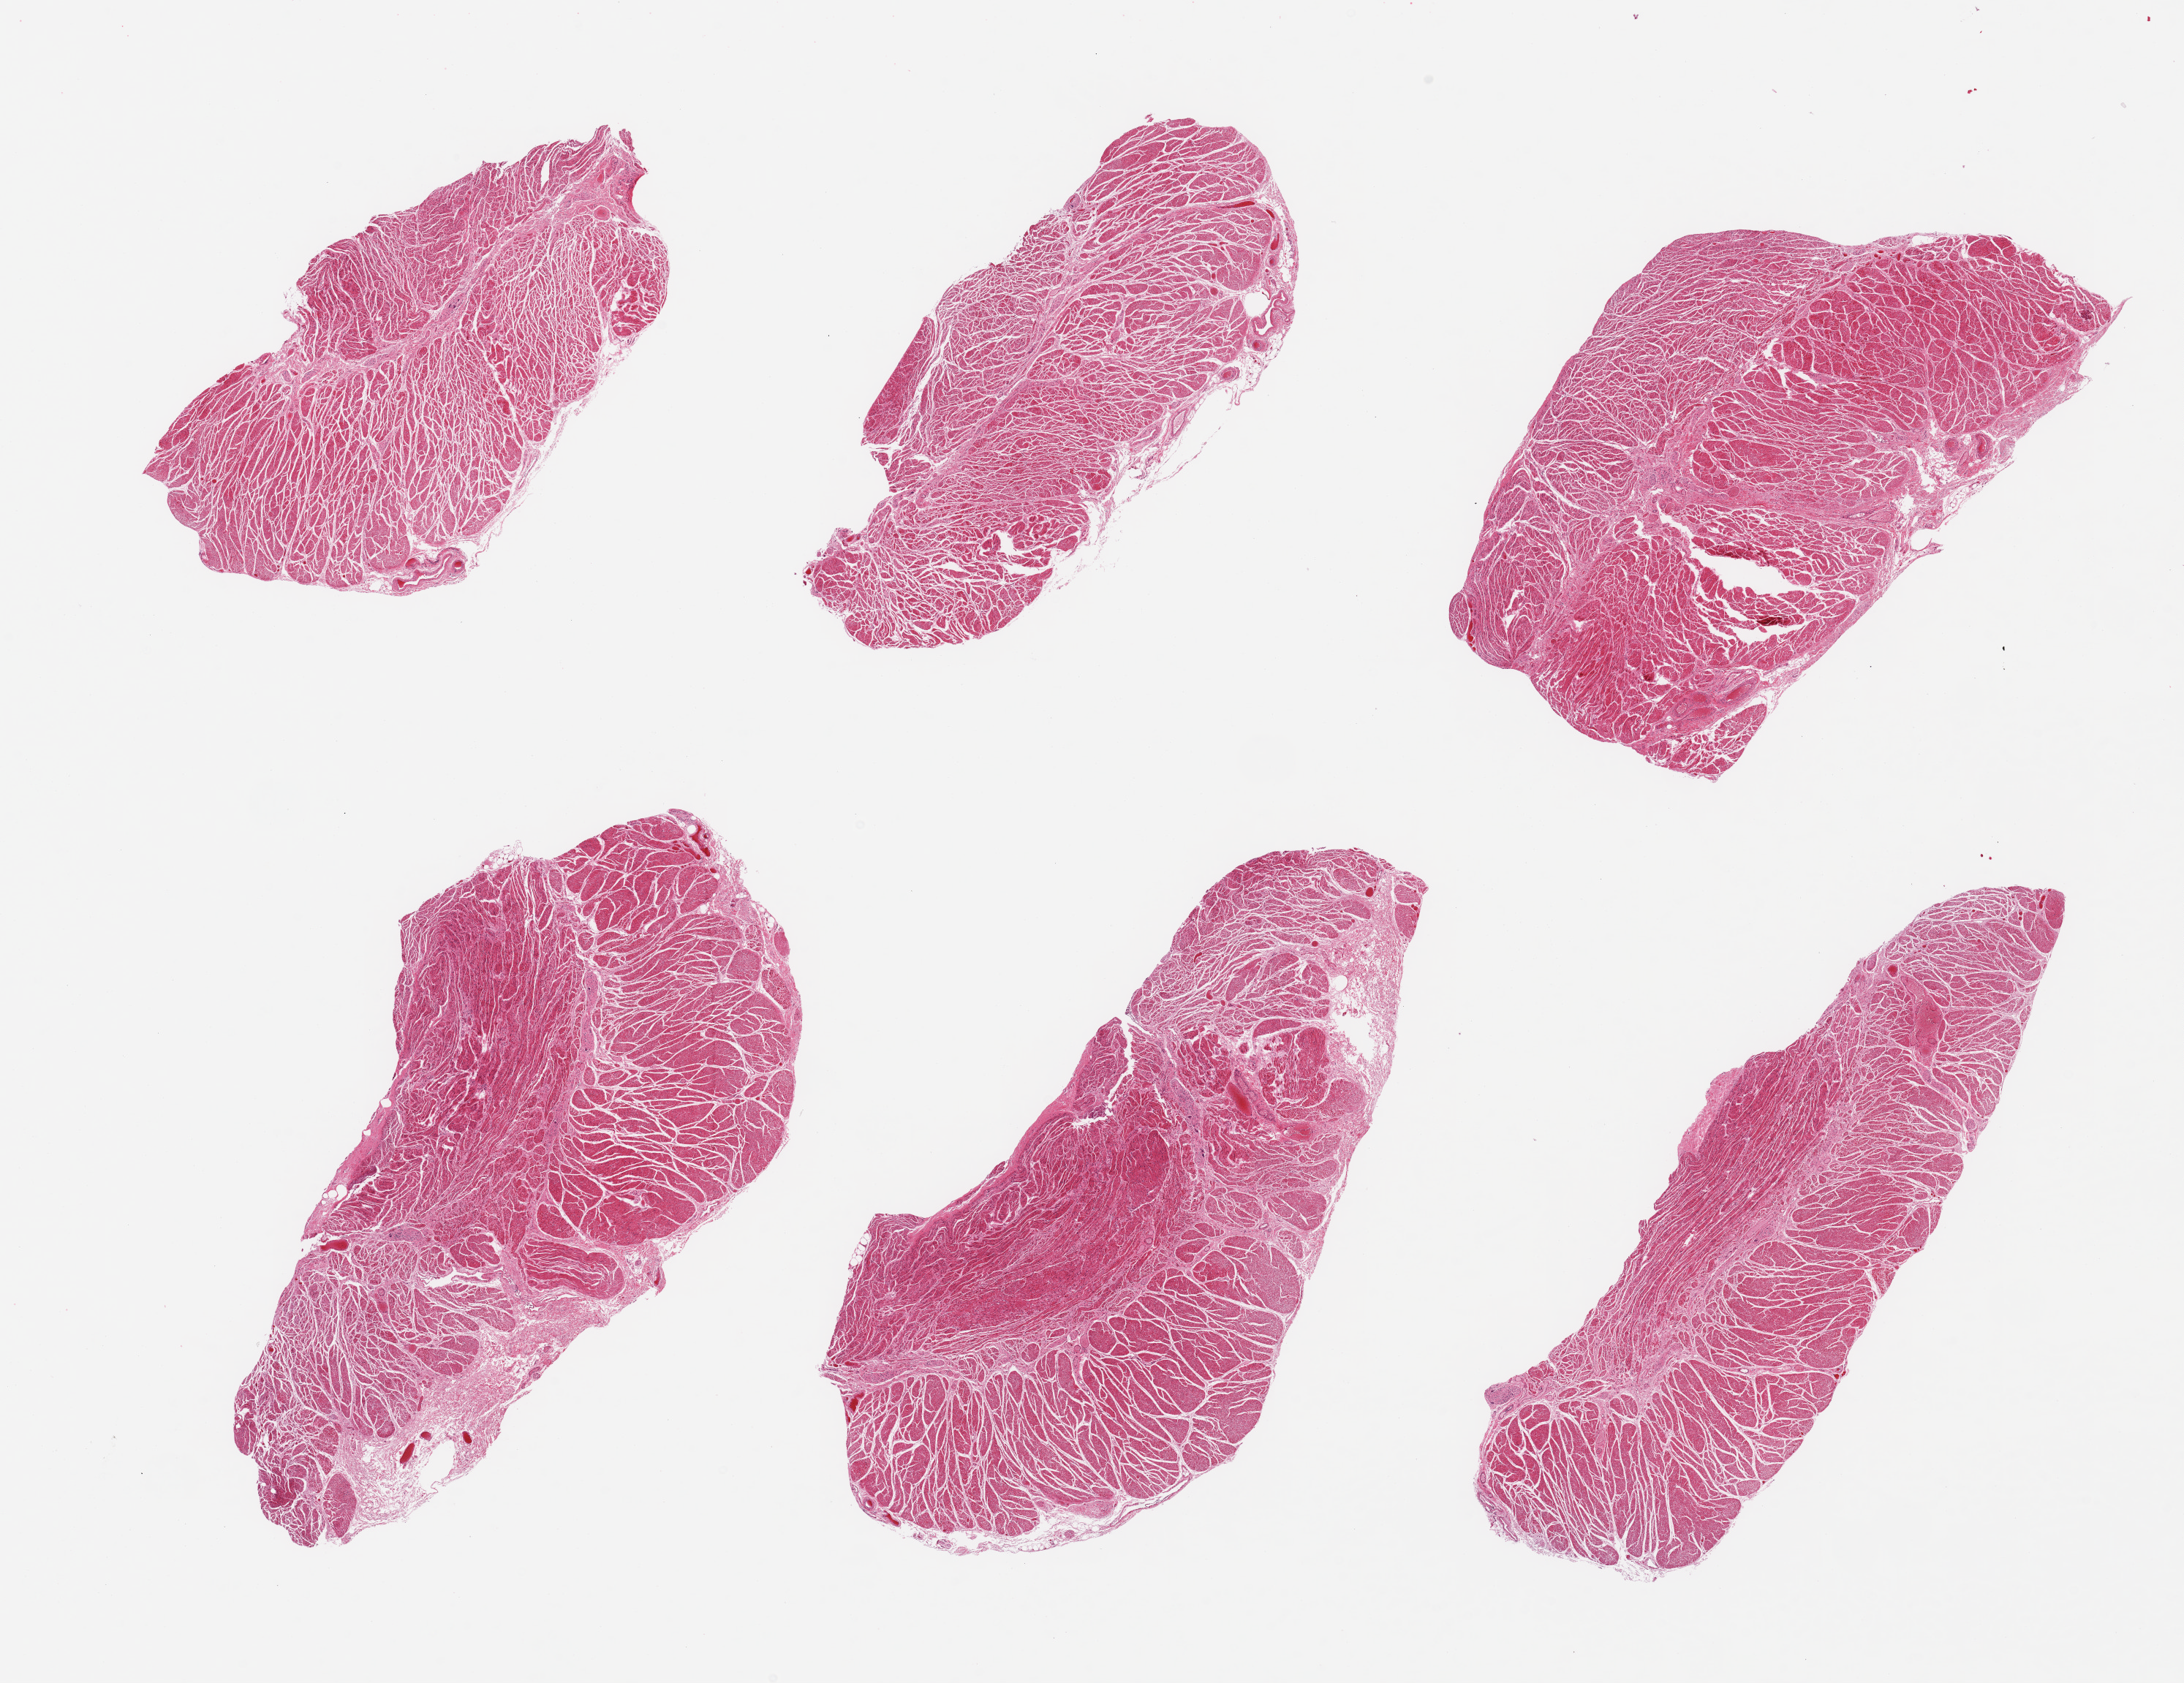
Digitized haematoxylin and eosin-stained section — low-resolution overview of the scanned area, about 23.6 x 18.2 mm. PAXgene-fixed paraffin-embedded (PFPE) section. Target tissue: esophageal muscle. Donor tissue sample. Male donor.
Reviewer comment on this tissue sample: 6 pieces; confirmed target muscularis.